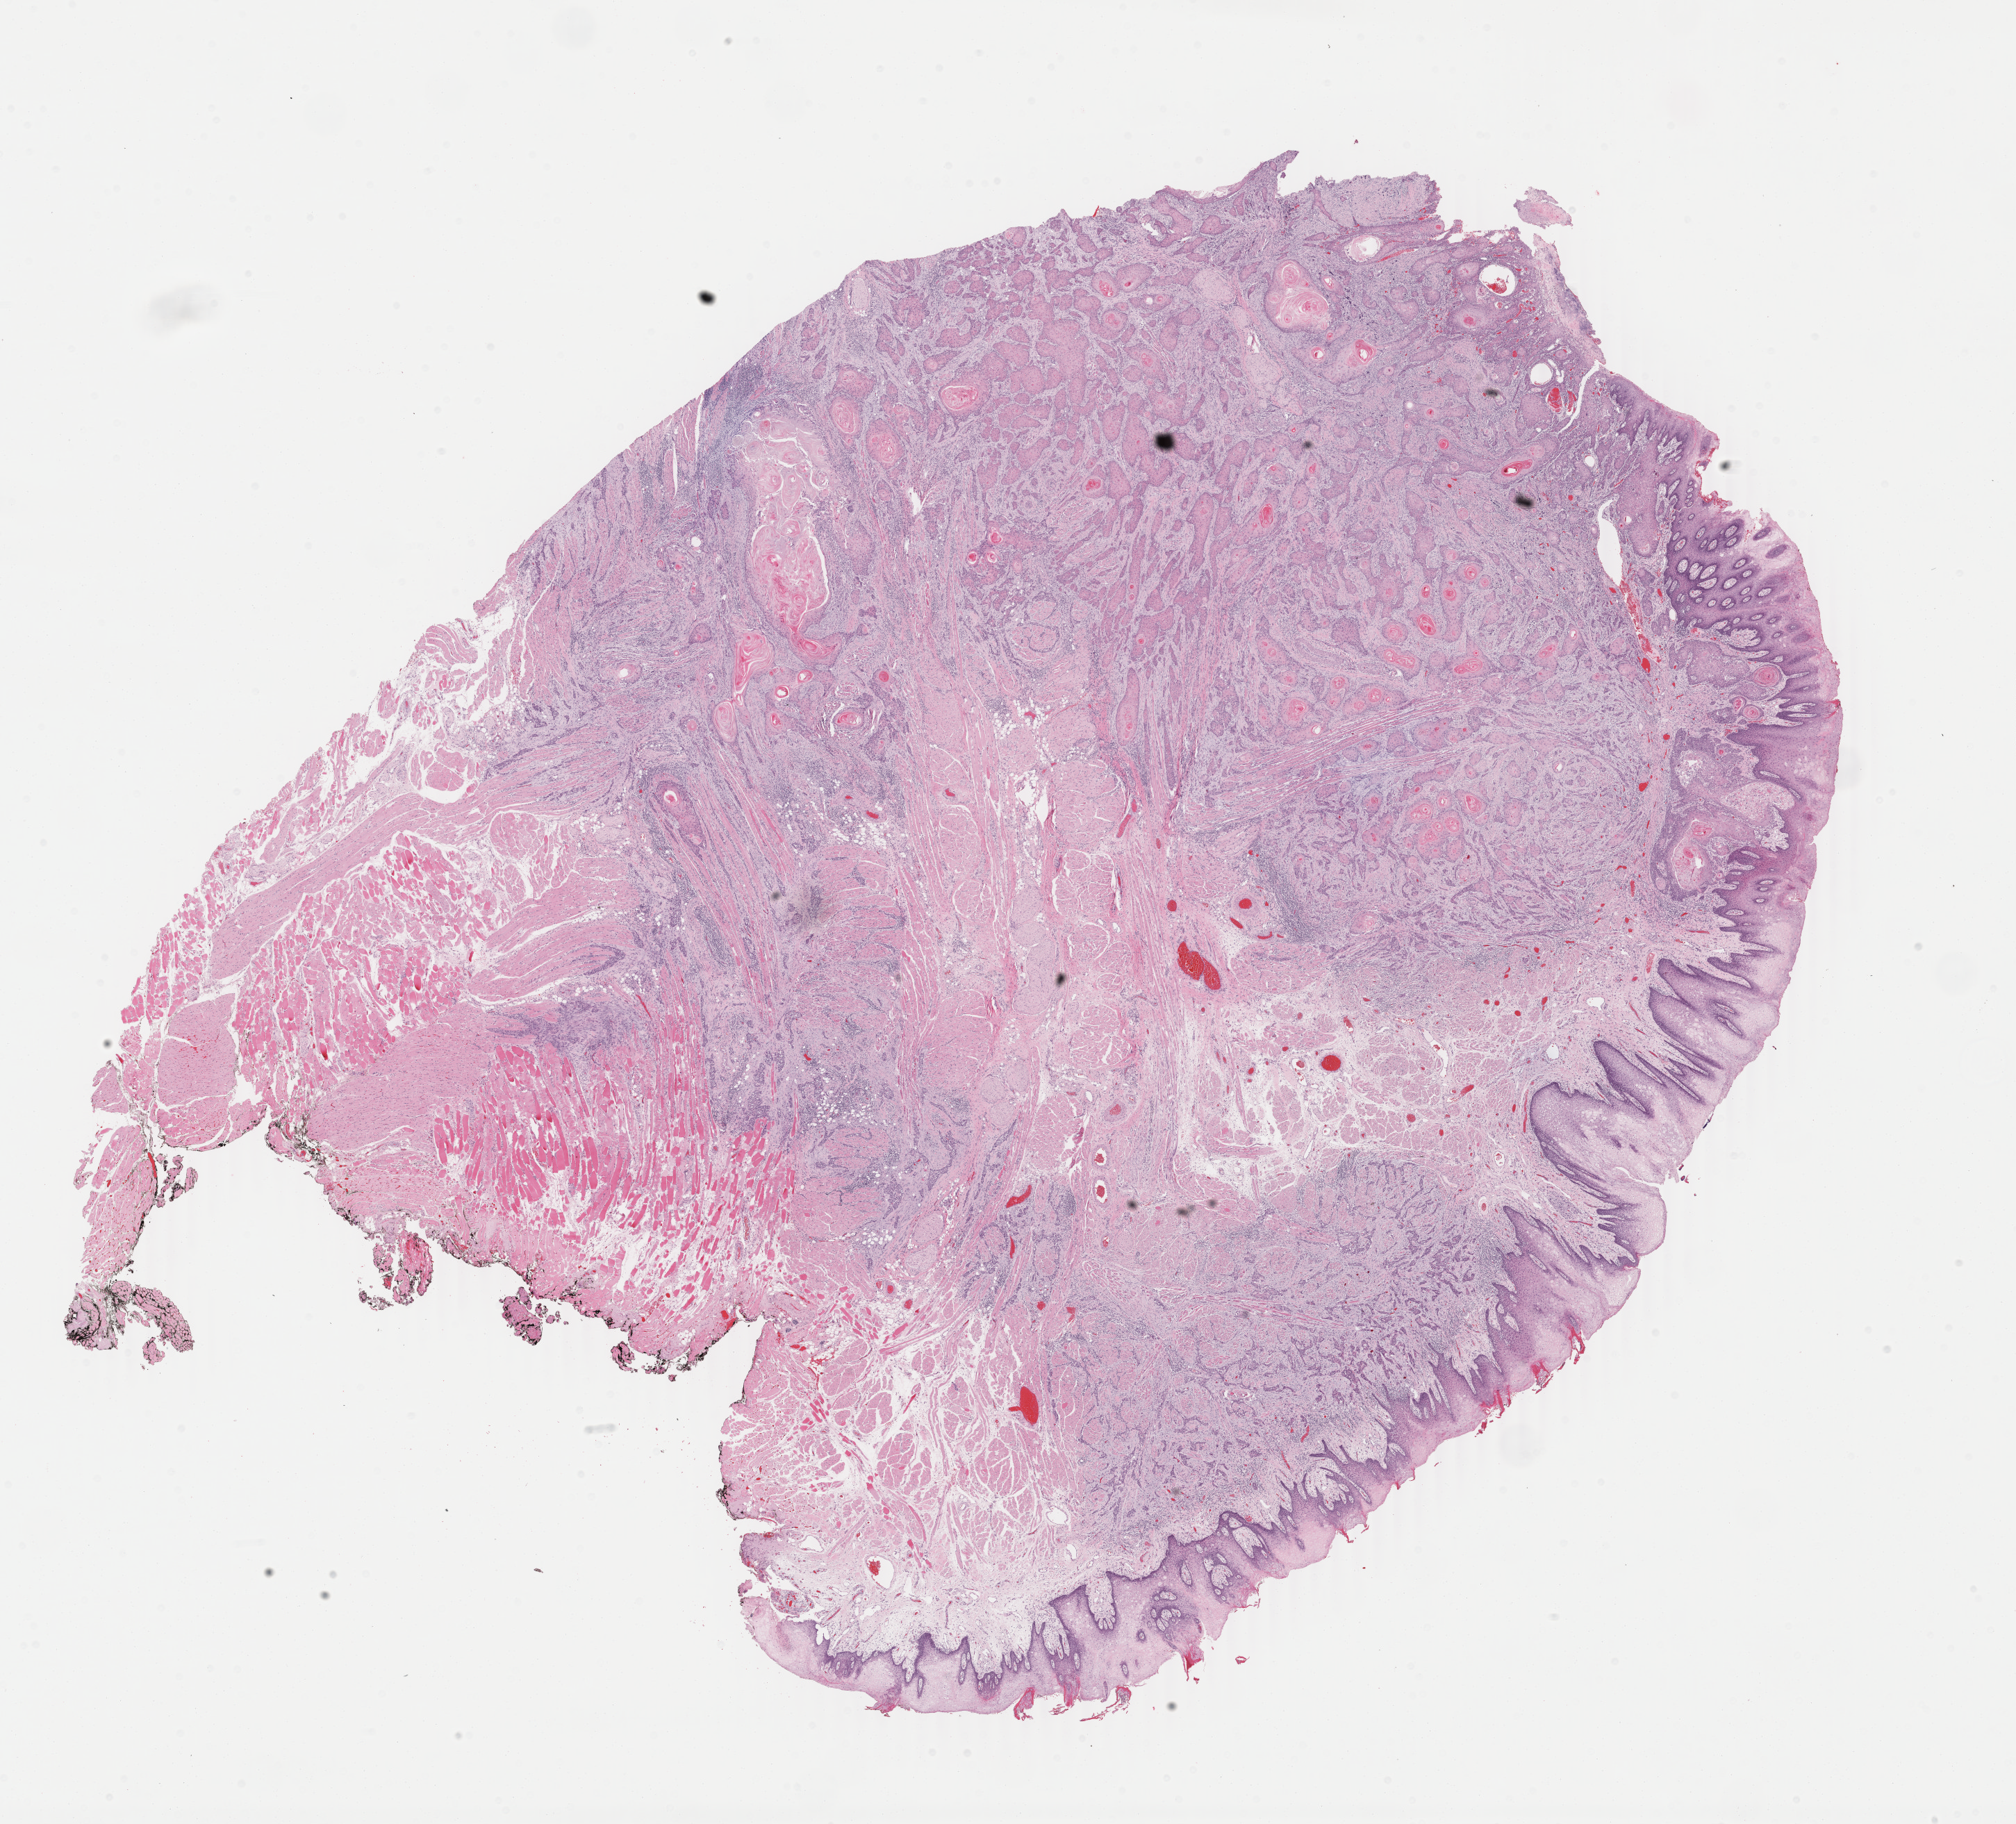
Hematoxylin and eosin (H&E) stained whole-slide image, low-resolution overview of the scanned area, about 23.1 x 20.9 mm (slide scanned at 40x), FFPE section, head and neck, primary tumour sample. Patient: male, age at initial diagnosis 54 years. Histologic grade: G1 (well differentiated).
* diagnosis: Squamous cell carcinoma, keratinizing, NOS (tongue, NOS)
* TNM: T2 N2b M0
* AJCC pathologic stage: IVA (7th edition)
* lymph nodes positive (case pathology): 2 of 73 examined